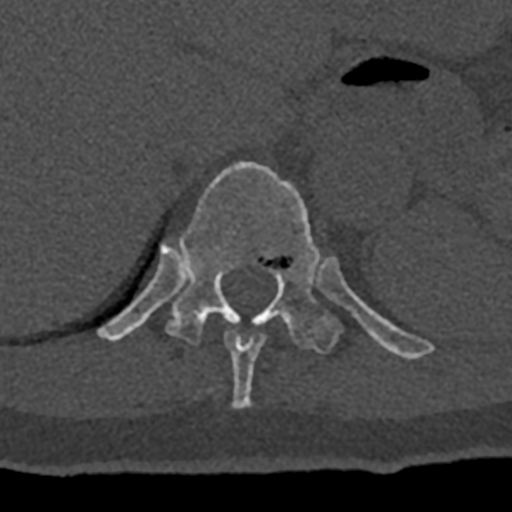
CT including the spine, one axial slice. Slice 564 of 797 in the series (ordered by position). Bone window (W 1800 / L 400 HU). 0.5 mm slice thickness. 512 × 512 image matrix, field of view 160 × 160 mm. Male patient, age 74 years. From the clinical record (not read from this slice): primary cancer: renal; vertebrae with lytic lesions (as recorded): T10, L1, L2, L3, L4, L5.
Annotated regions visible in this slice (semi-automatically segmented with operator editing):
- T10 vertebra: bounding box <224,330,266,409> (left, top, right, bottom; pixels)
- T11 vertebra: <97,161,432,360>